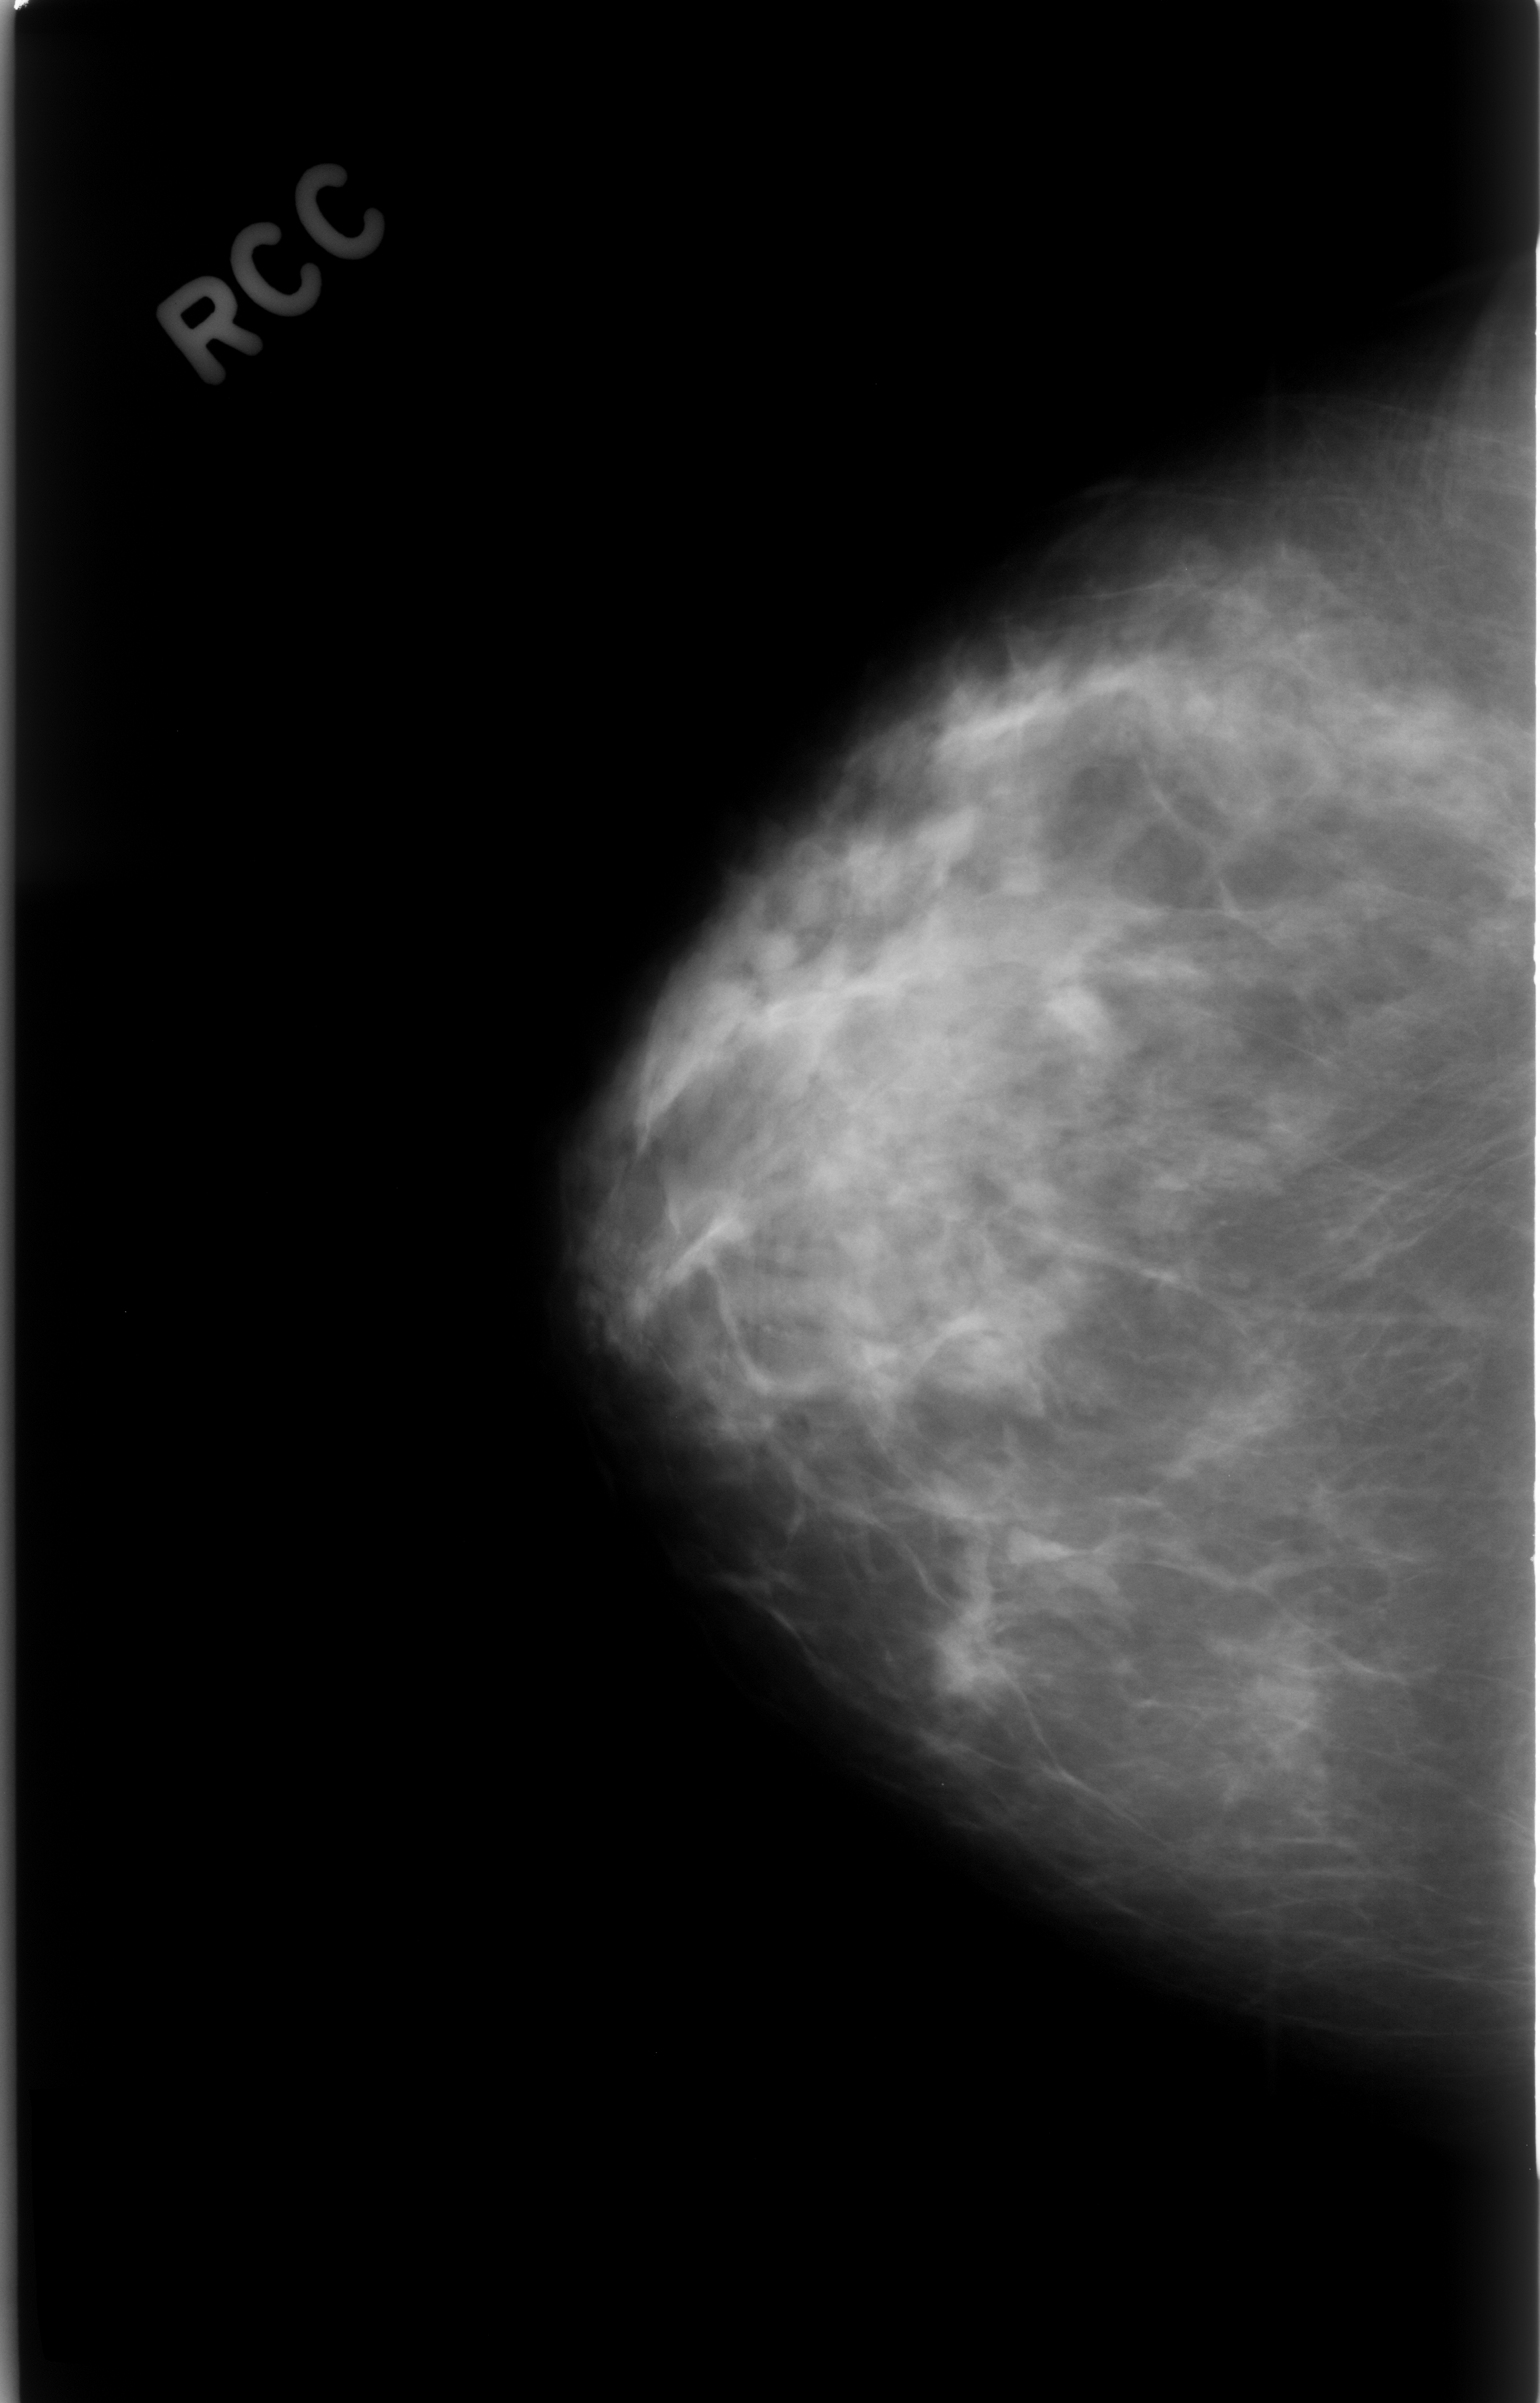
Mammogram (digitized film), right breast, CC view.
Finding: mass, shape irregular, margins spiculated; BI-RADS assessment category 3; benign without callback (not worked up further).